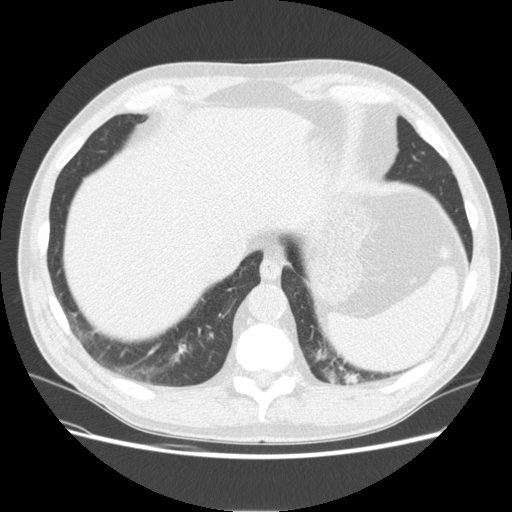
Low-dose screening chest CT, one axial slice. Position 44 of 165 along the scan axis. Reconstruction kernel STANDARD. Lung window (W 1500 / L -600 HU). 2.5 mm slice thickness. 512 × 512 image matrix, field of view 375 × 375 mm.
Annotated regions visible in this slice (outlined manually by an expert reader):
- lesion 1 (tumor, upper lobe of left lung): bounding box [x1, y1, x2, y2] px = [315, 350, 361, 386]